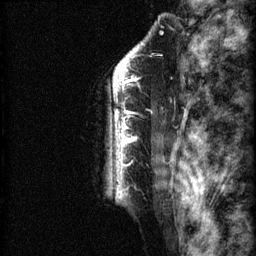
Breast MRI (dynamic contrast-enhanced), one sagittal slice. Position 55 of 60 along the scan axis. 3 images stored at this slice position (order not interpretable as contrast timing). 1.5 T. TE 4.2 ms, TR 22.7 ms. 2 mm slice thickness. 256 × 256 image matrix, field of view 180 × 180 mm. Patient: female, 48 years. From the clinical record (not read from this slice): setting: breast cancer imaged before/during neoadjuvant chemotherapy; receptor status: triple-negative.
Structures marked on this image (semi-automatically segmented with operator editing):
- analysis volume of interest (the breast-tissue region the enhancement analysis was run in; not a lesion): bounding box (x1, y1, x2, y2) in pixels: (86, 30, 173, 207)
- tumour enhancement mask (voxels above the 90 % enhancement threshold inside the analysis volume of interest): (108, 43, 143, 195)